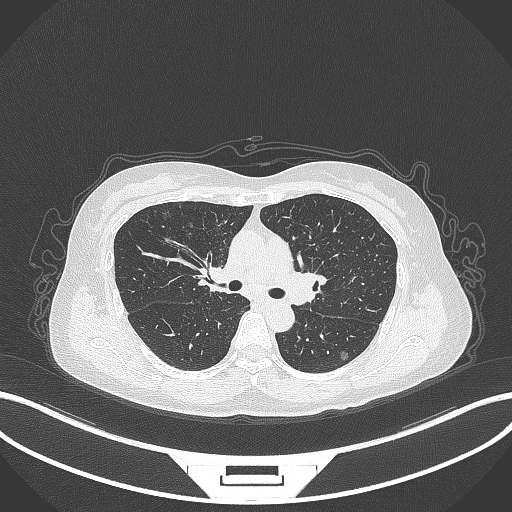
Chest CT, one axial slice. Position 204 of 315 along the scan axis. Reconstruction kernel B70f. 120 kVp. Lung window (W 1500 / L -600 HU). 1 mm slice thickness. 512 × 512 image matrix. Patient: female, 61 years. From the clinical record (not read from this slice): clinical TNM (as recorded): T1b N0 M0; histopathological grade: G1.
Annotated regions visible in this slice (rectangle marked by the reading radiologist):
- lung tumour (recorded histology: adenocarcinoma): box from (x=157, y=208) to (x=176, y=222) px